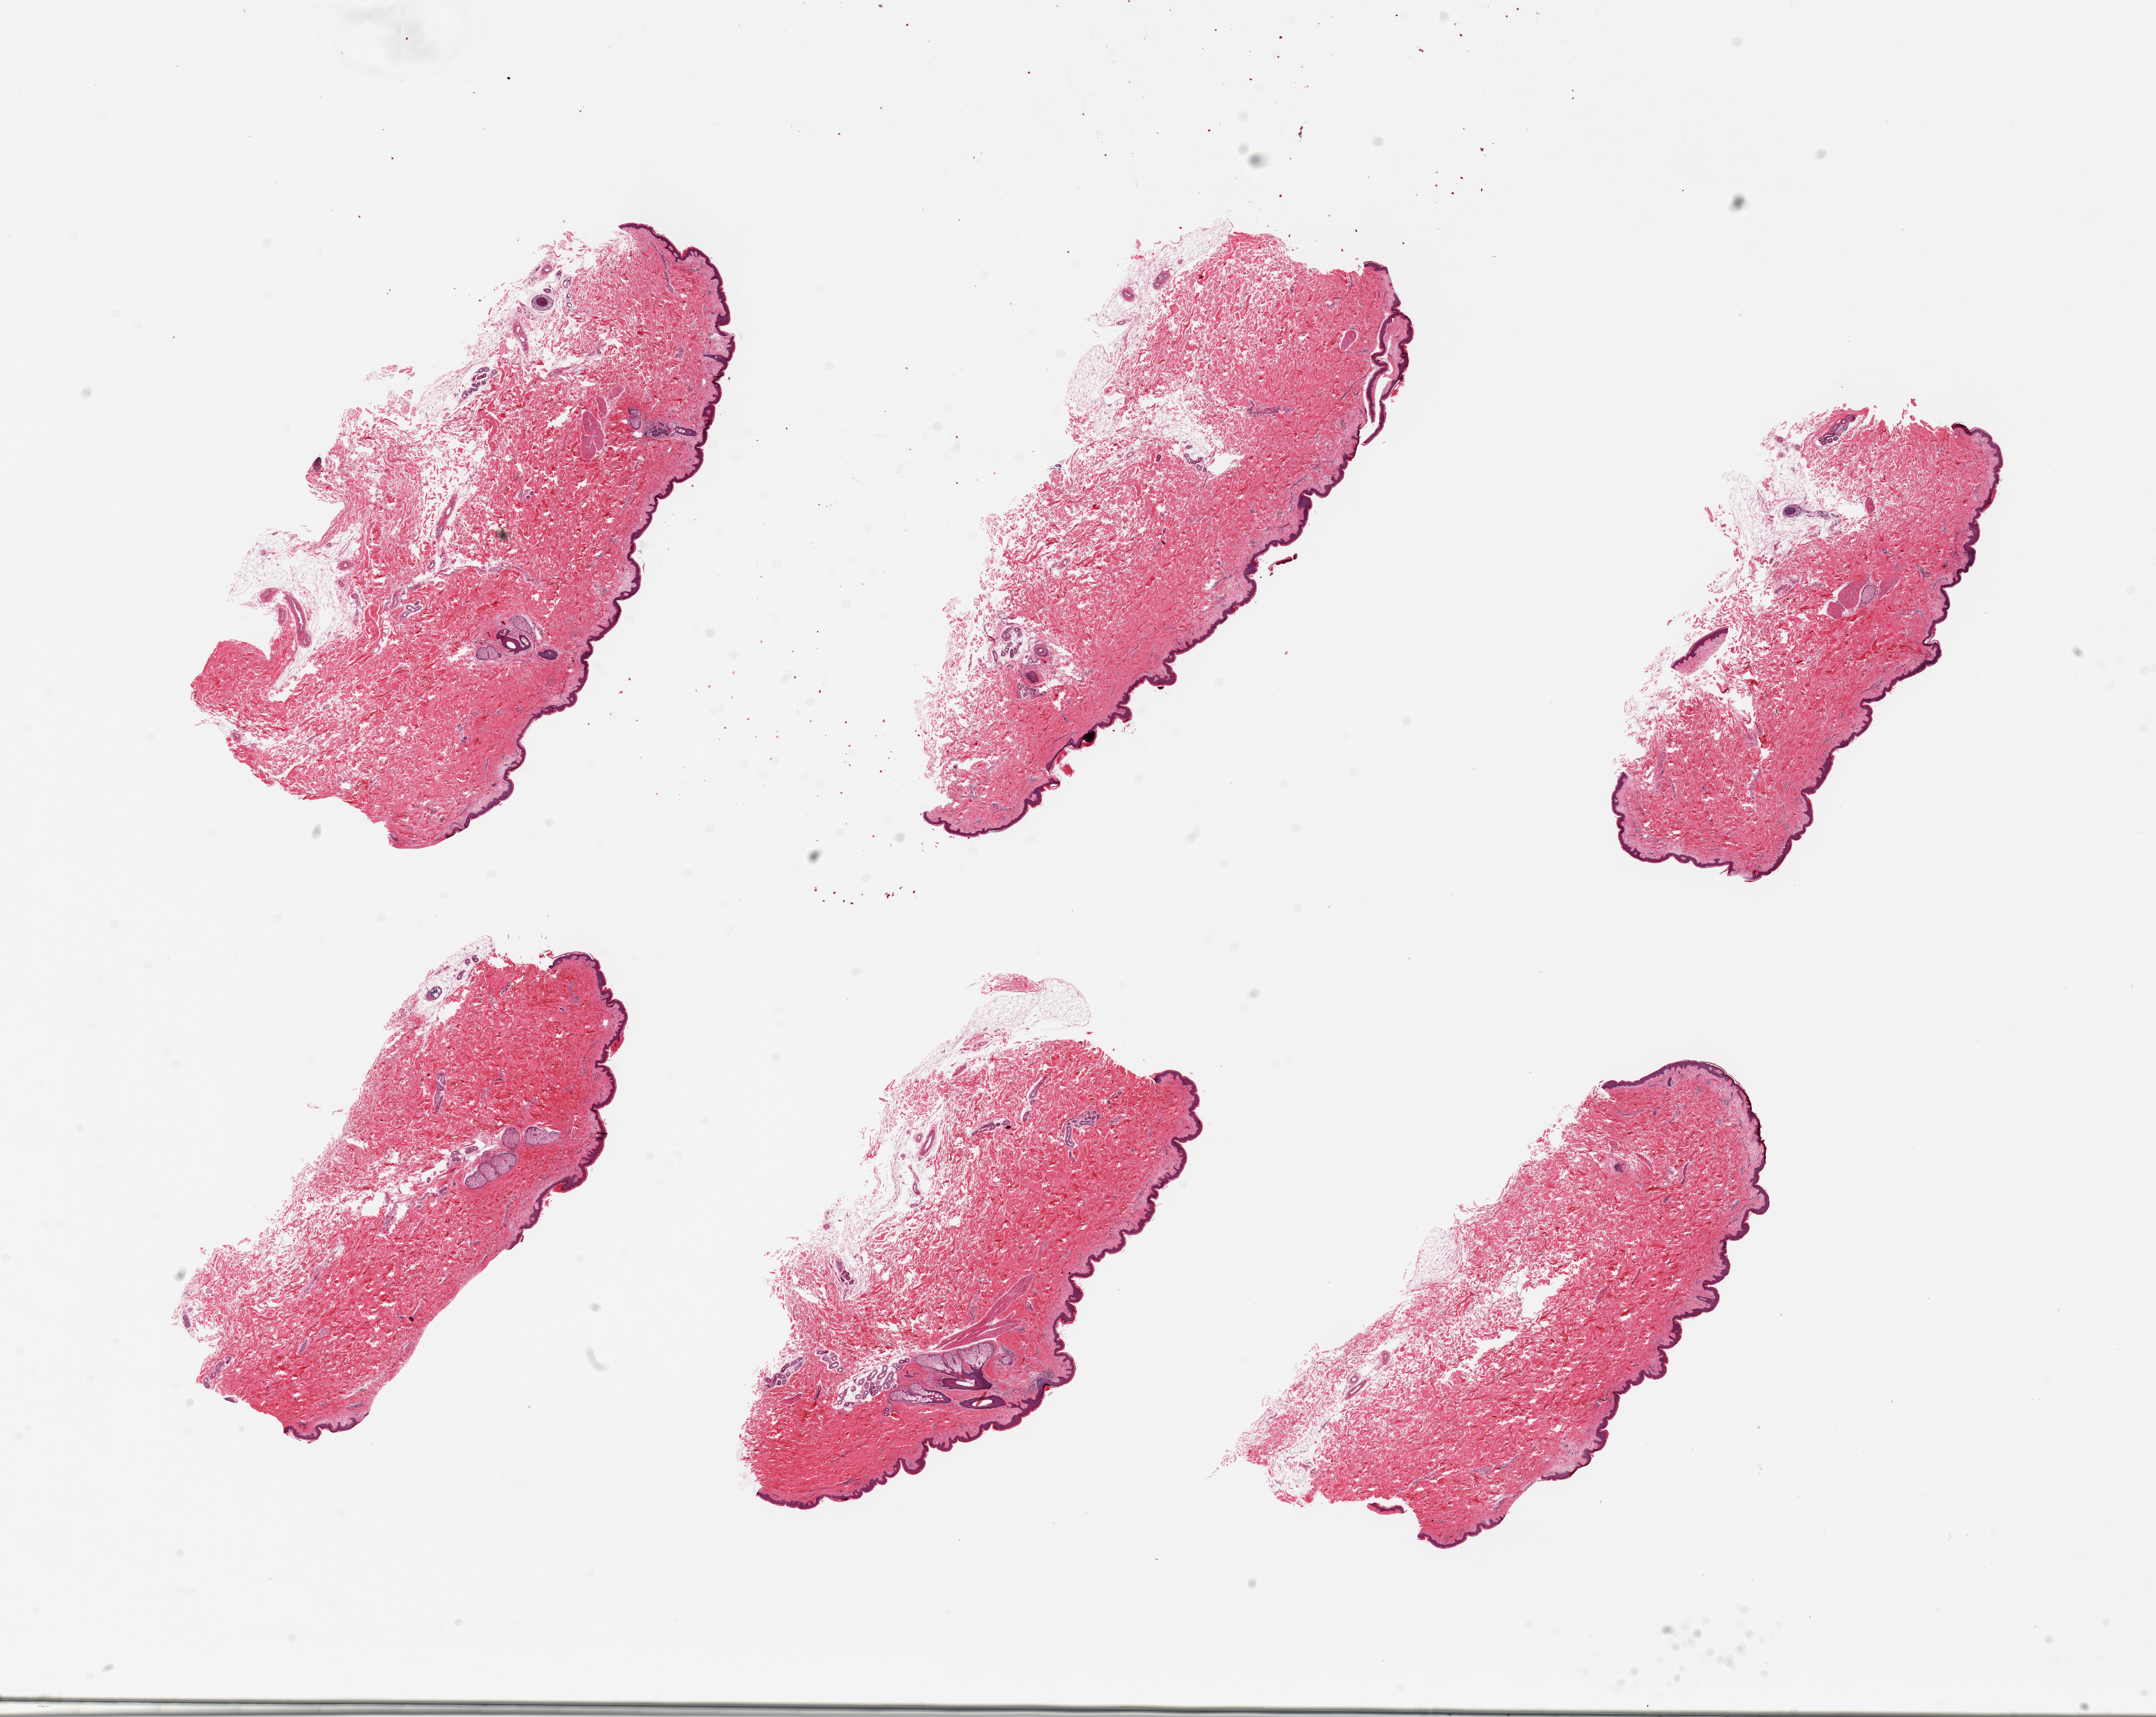
H&E whole-slide image, brightfield, low-resolution overview of the scanned area, about 26.6 x 21.2 mm; PAXgene-fixed paraffin-embedded (PFPE) section; target tissue: skin of suprapubic region; tissue donor sample. Donor: male.
Pathologist's review note for this sample: 6 pieces, up to 8x5mm; well dissected.